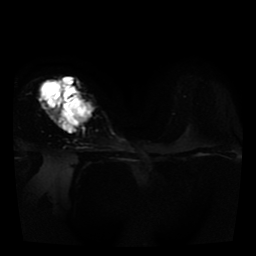
Breast MRI, one axial slice. Slice 27 of 41 in the series (ordered by position). Diffusion-weighted series; image 2 of 4 stored at this slice position (different b-values; order by instance number). 1.5 T. 5 mm slice thickness. 256 × 256 image matrix, field of view 330 × 330 mm. Female patient.
Structures marked on this image (outlined manually by an expert reader):
- tumour on diffusion-weighted imaging: bounding box (x1, y1, x2, y2) in pixels: (47, 78, 93, 133)